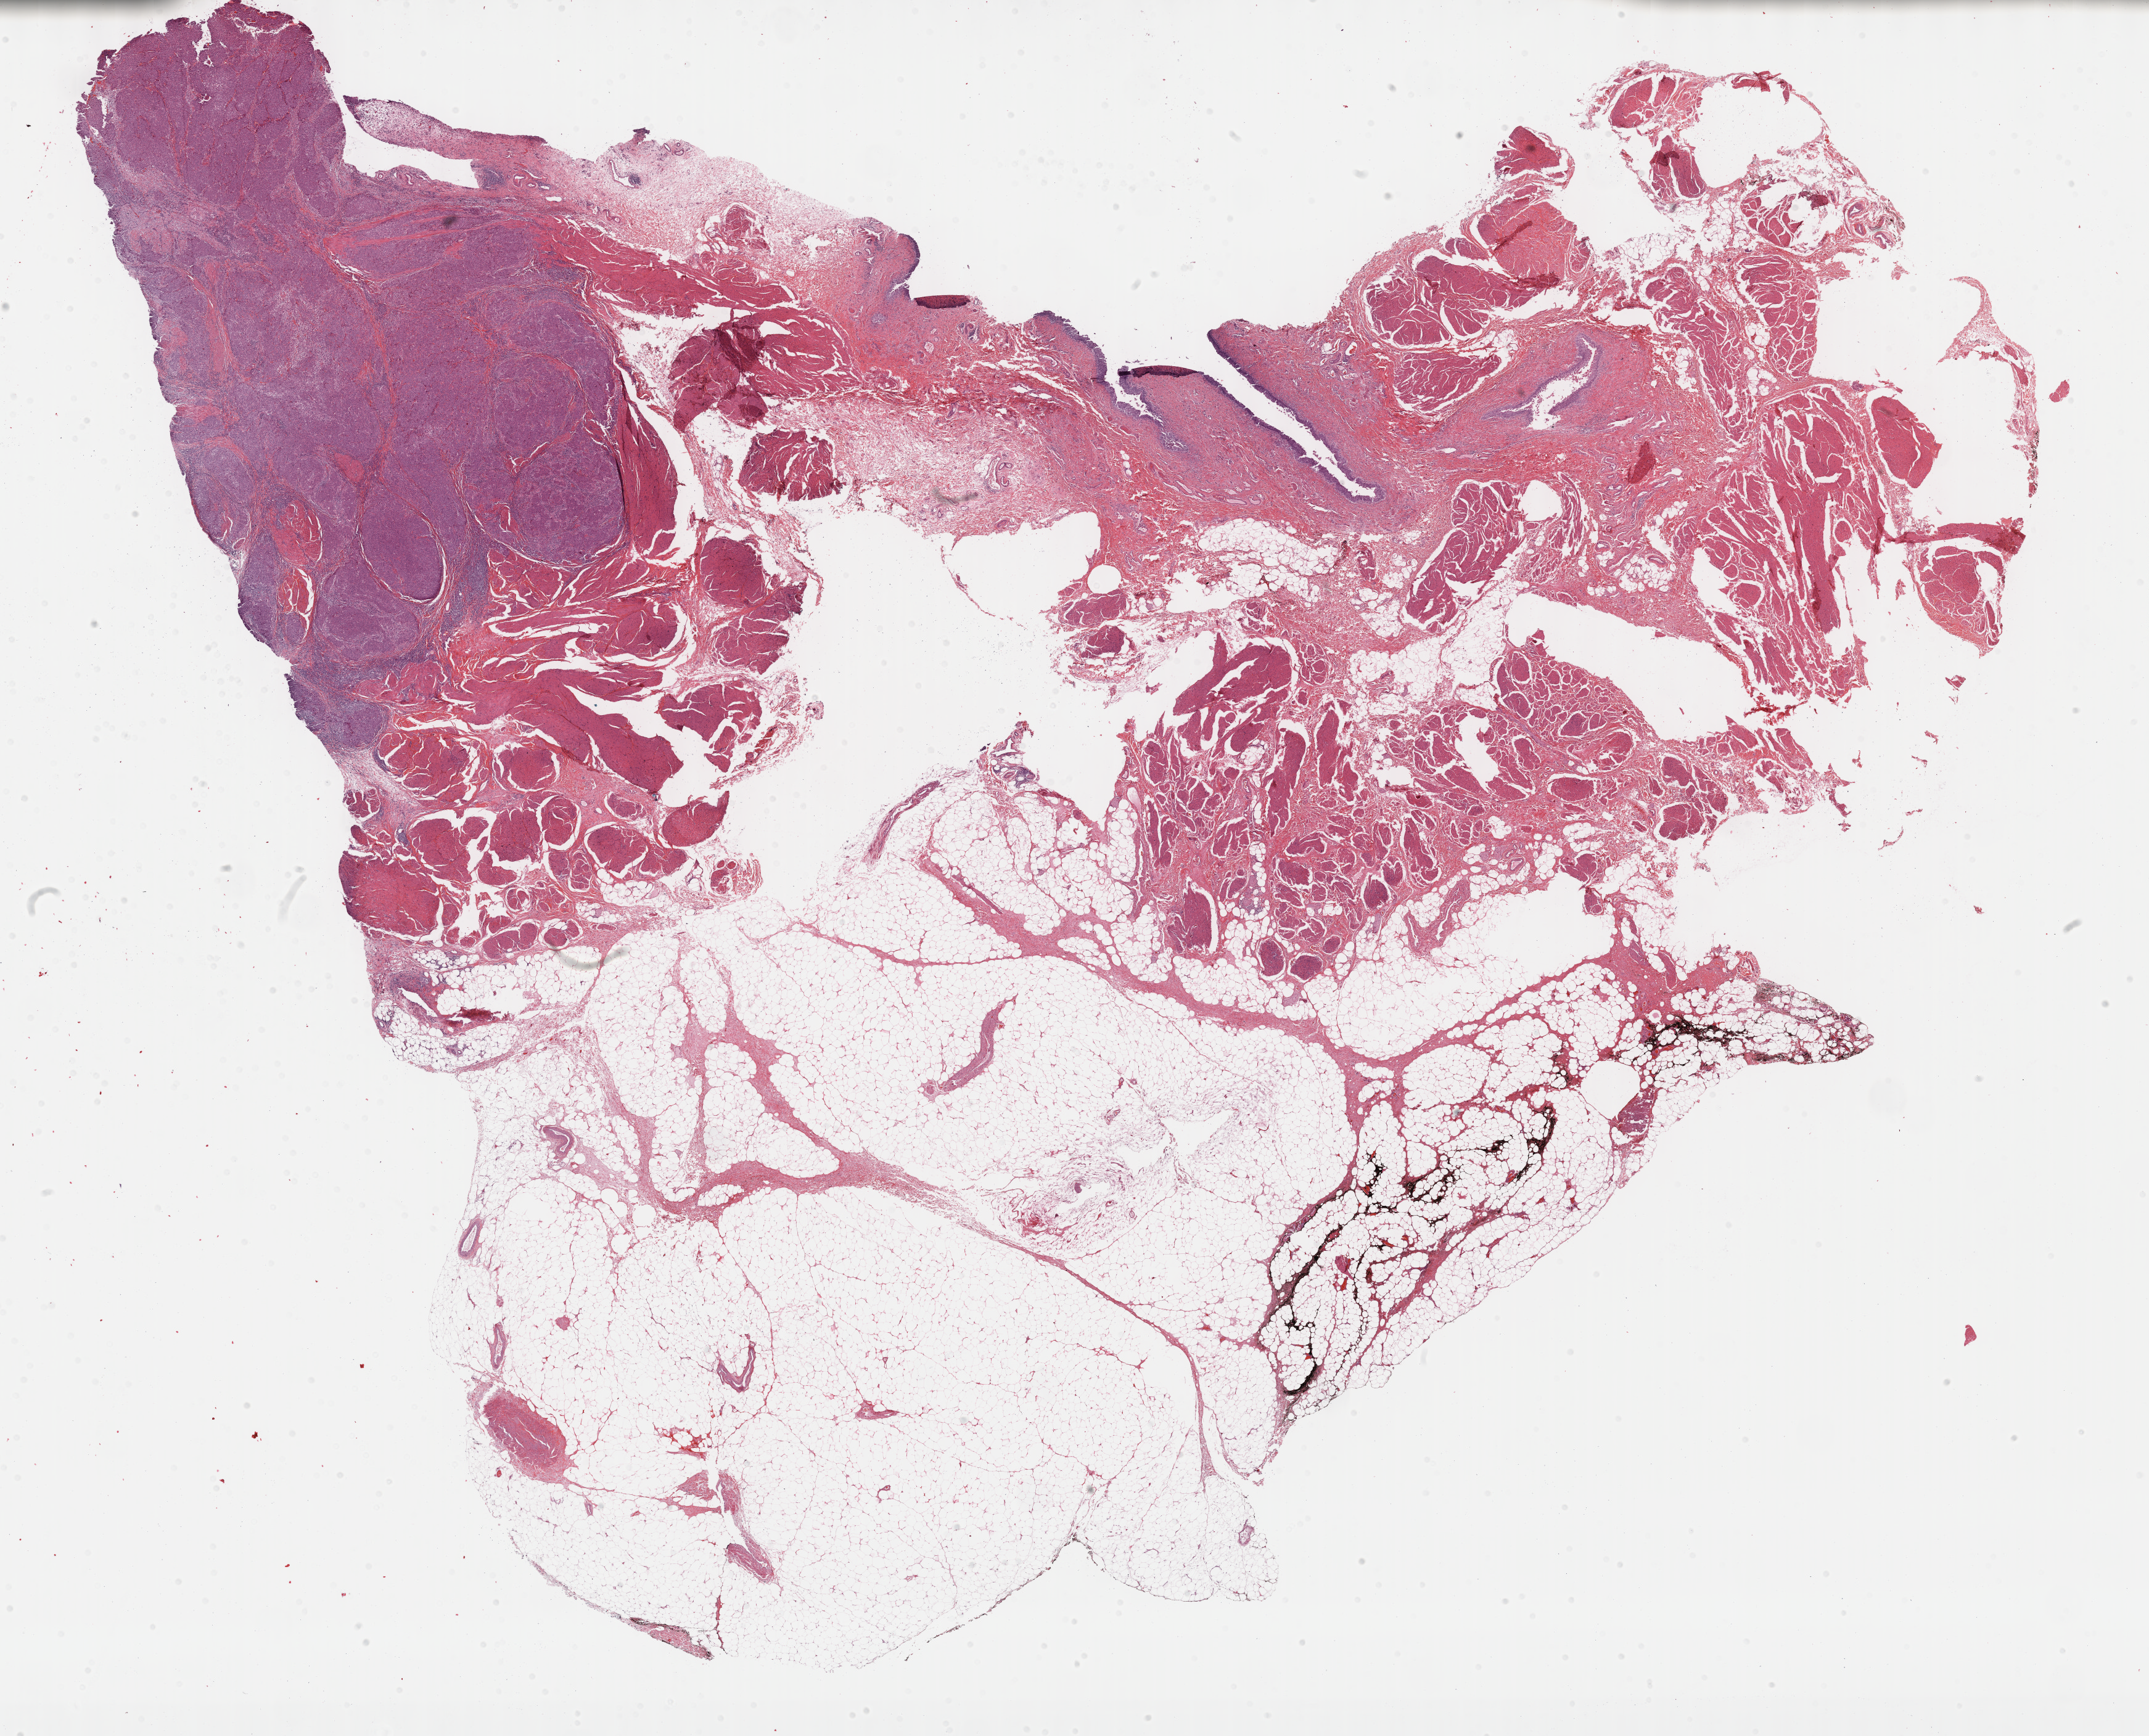
Digitized Hematoxylin and eosin (H&E) stained tissue section (whole slide), shown as a low-resolution overview of the whole scanned area (about 28.2 x 22.8 mm); formalin-fixed paraffin-embedded (FFPE) diagnostic section; bladder, primary tumour sample. Female, age 78 years at initial diagnosis. Histologic grade: high grade.
AJCC pathologic stage: IV. Diagnosis: Transitional cell carcinoma.